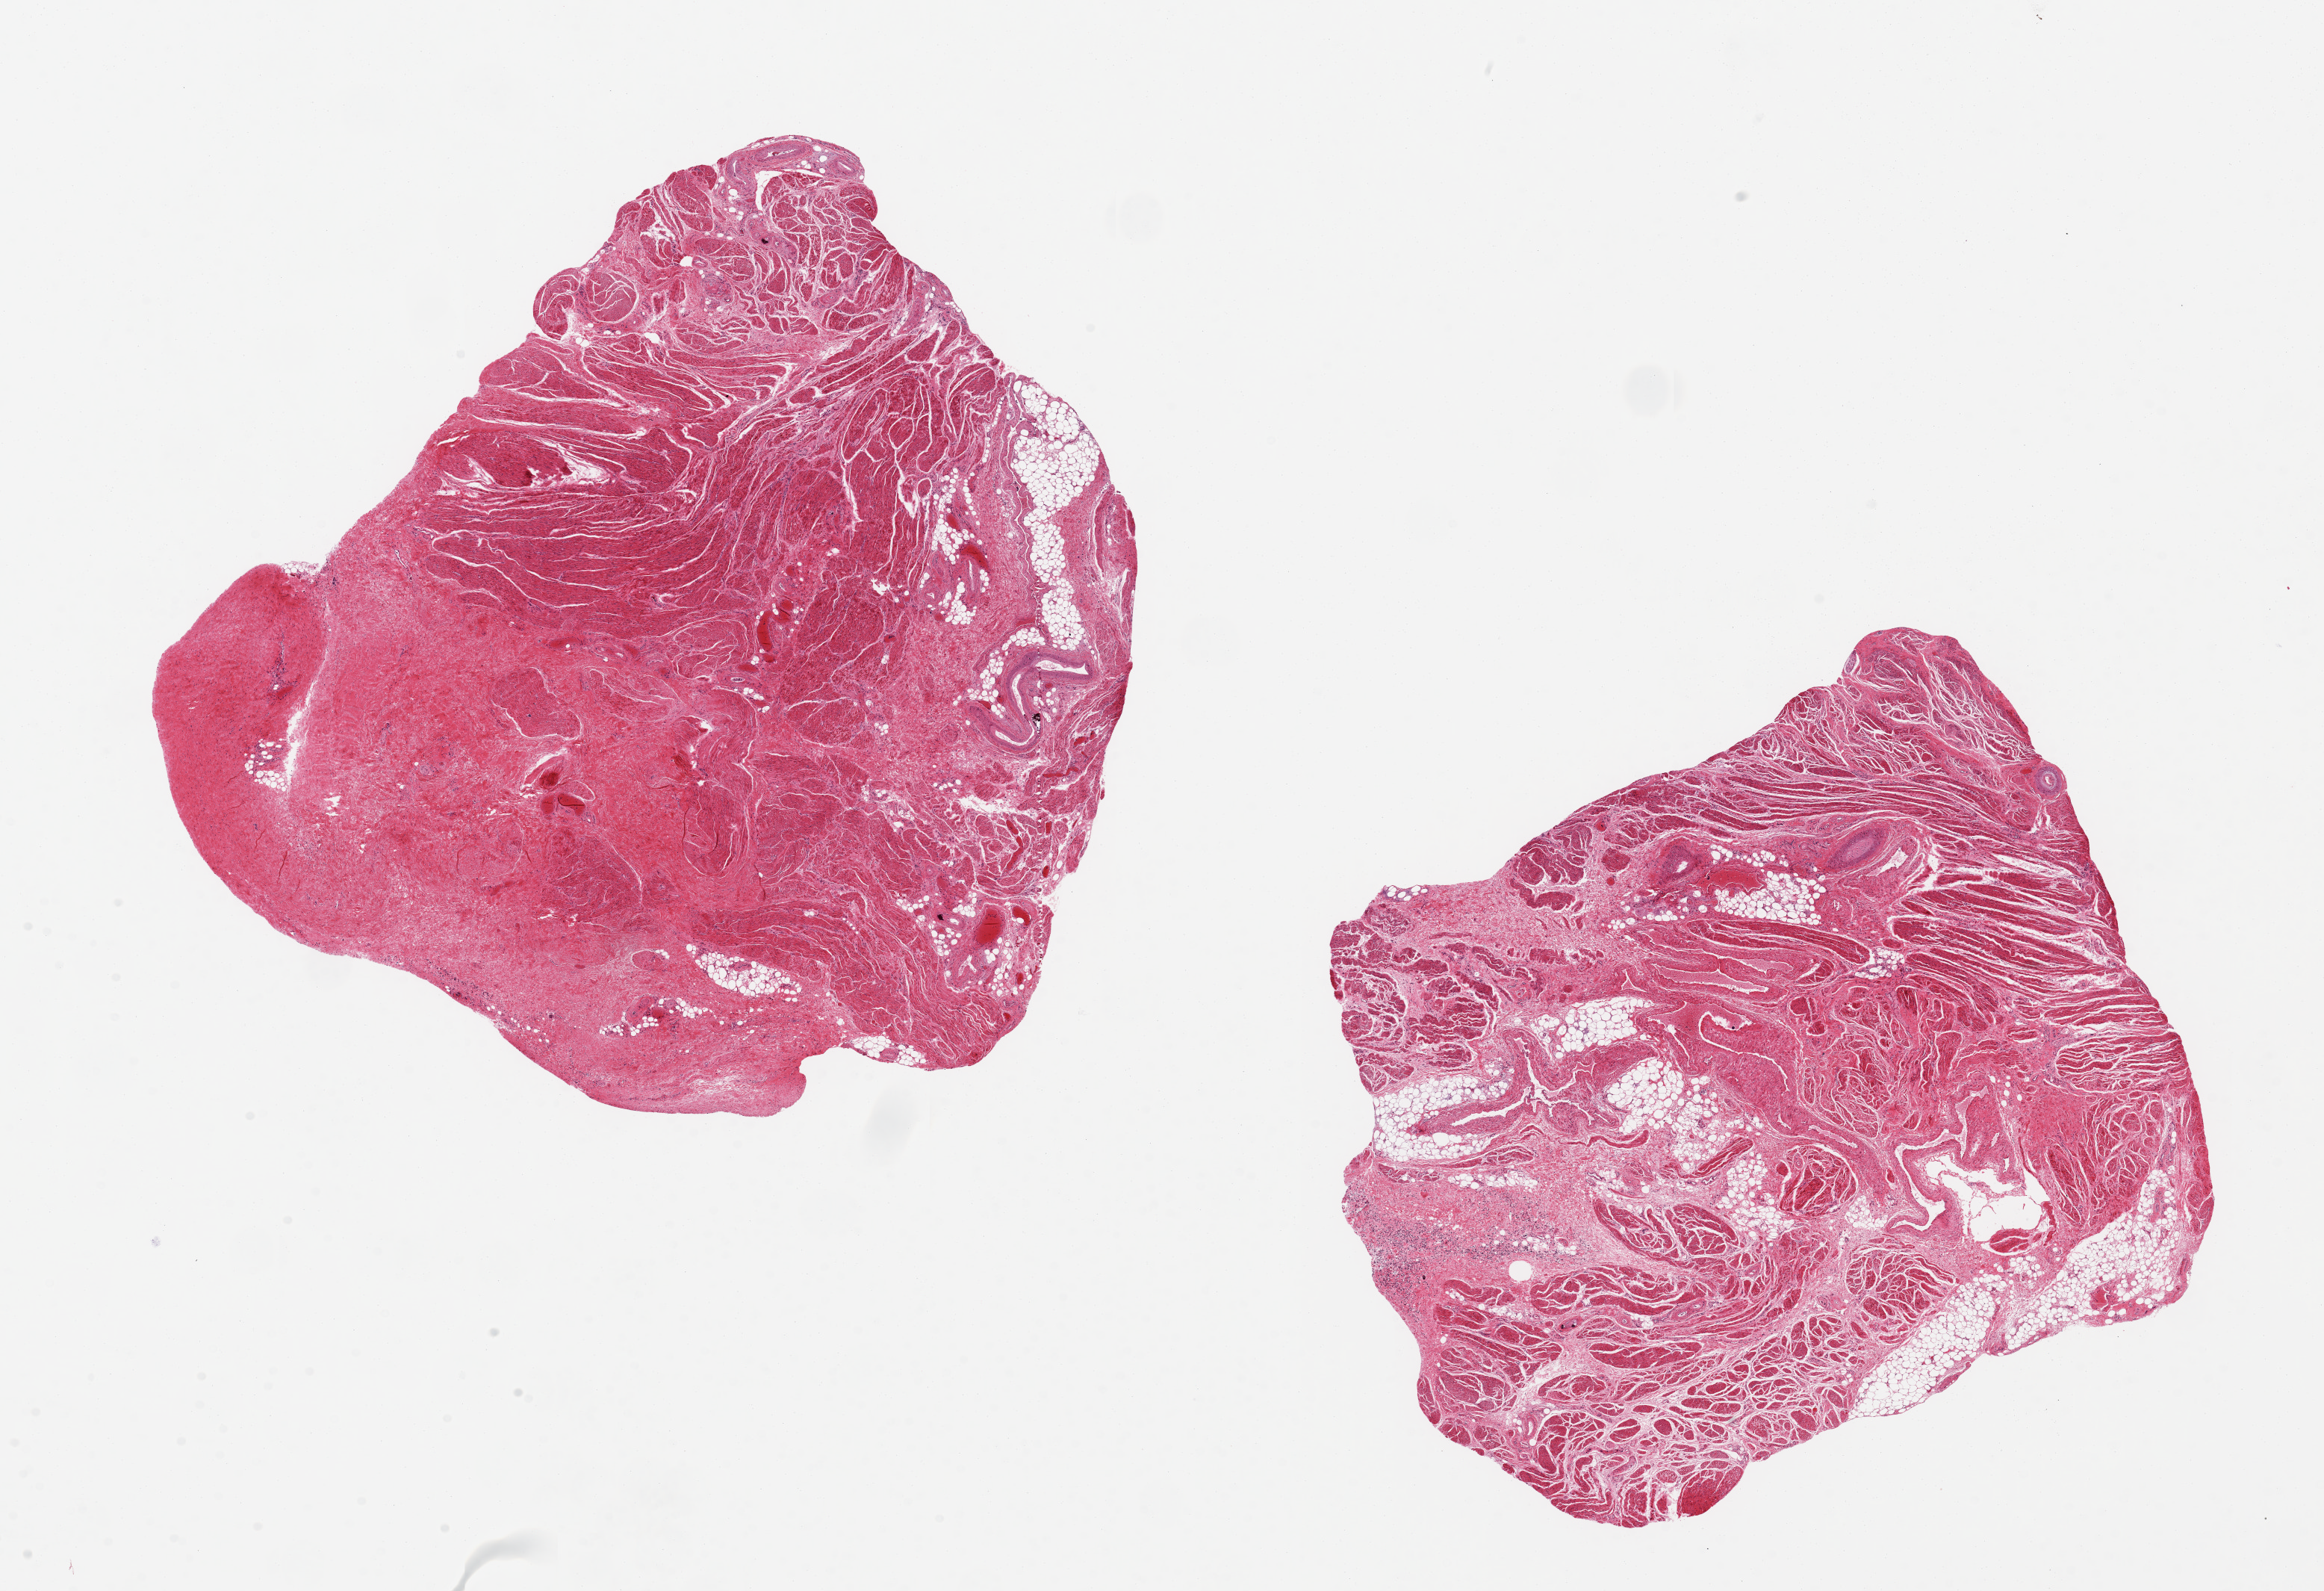
Hematoxylin and eosin (H&E) whole-slide image, a low-resolution overview of the entire scanned area, about 24.6 x 16.8 mm (acquisition: 20x scan); PAXgene-fixed paraffin-embedded (PFPE) section; target tissue: prostate; donor tissue sample. Donor sex: male.
Review note (as recorded): 2 pieces 10x8 & 8x7 mm; all muscle and fibrous, no glands; 10-20% adipose.